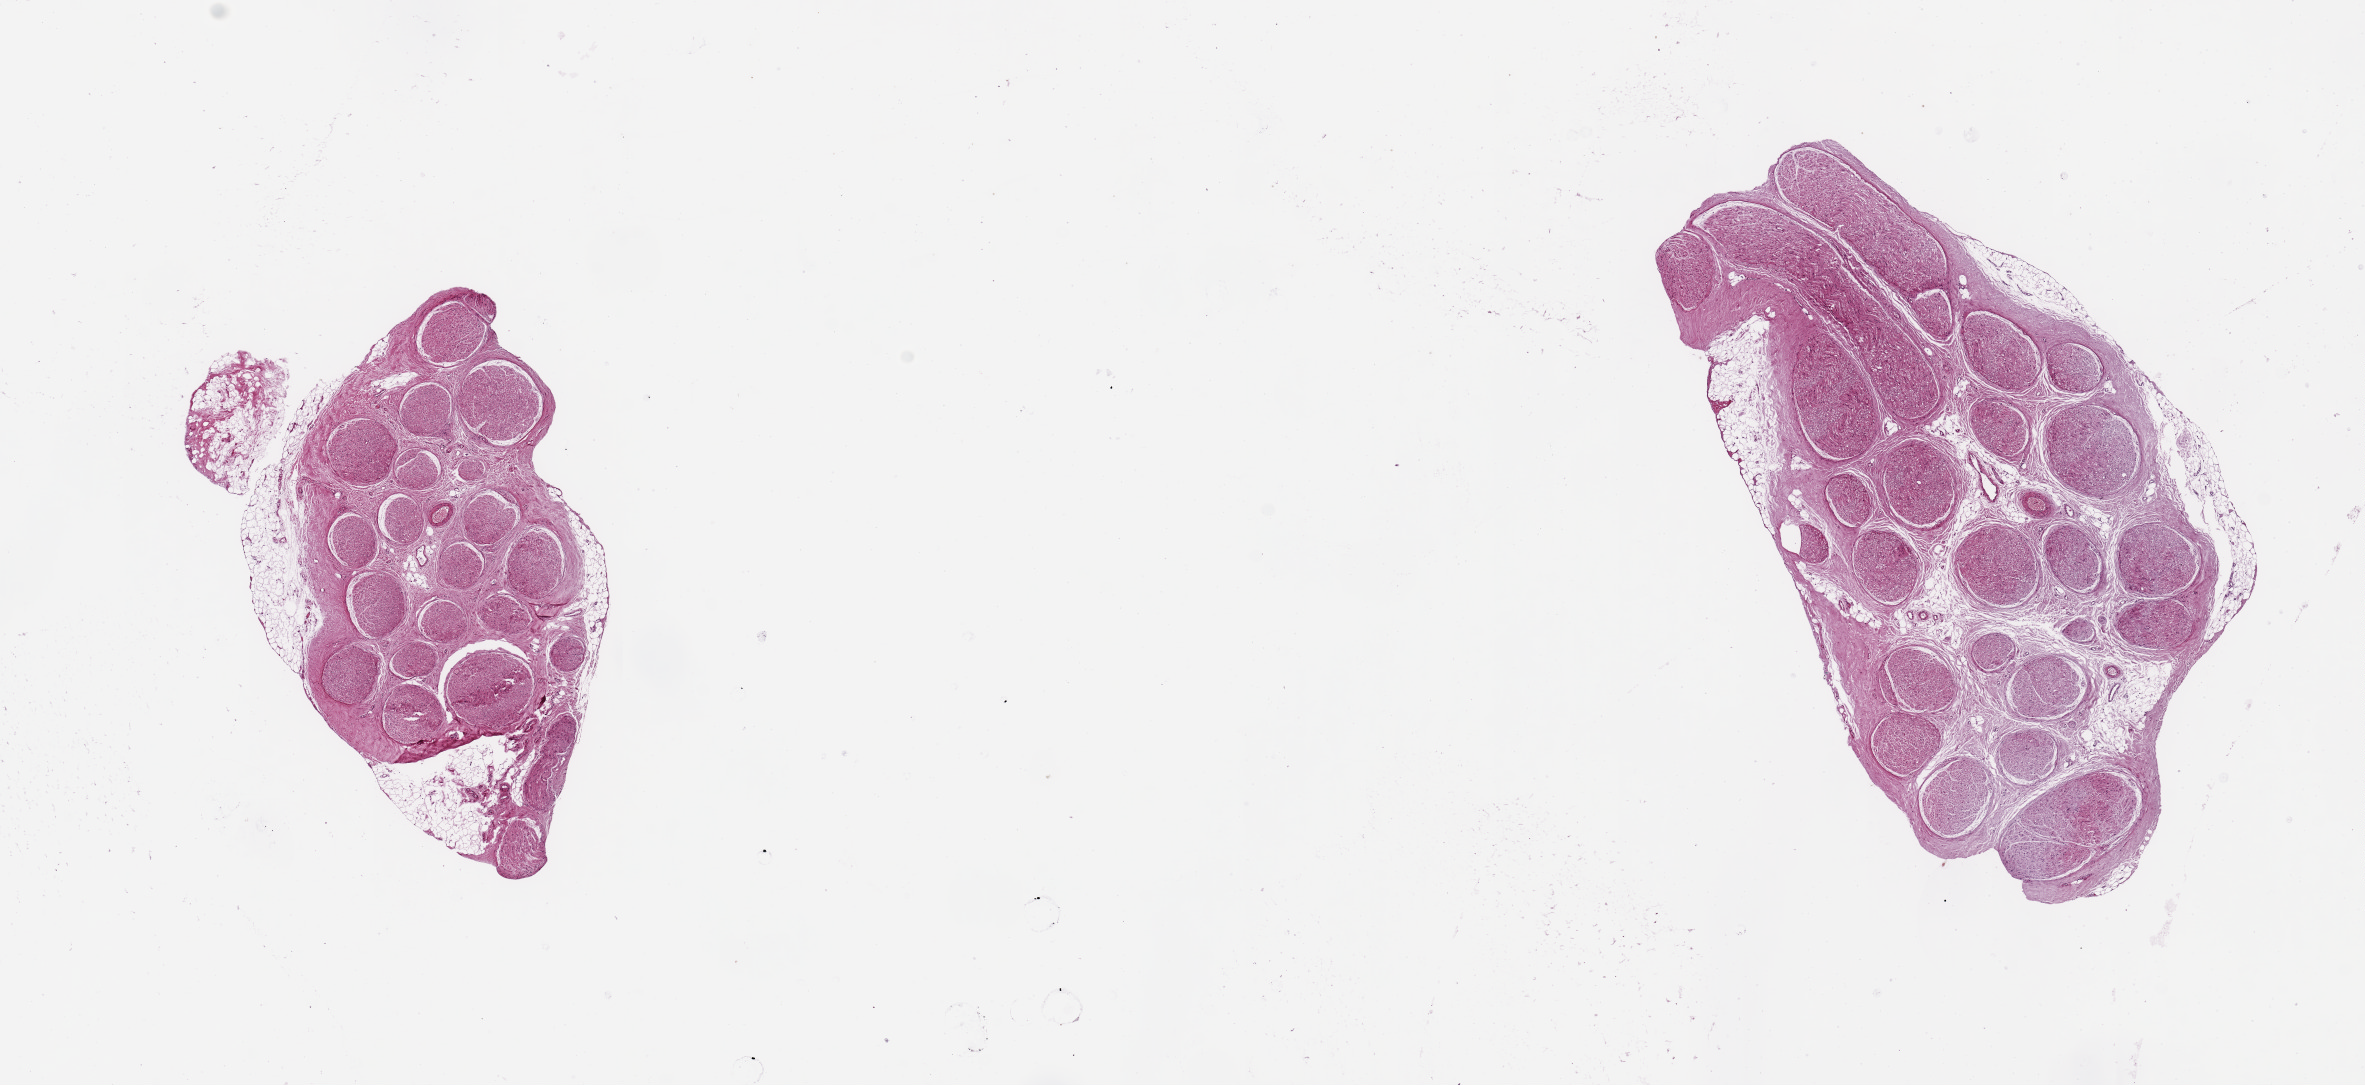
Whole-slide image, hematoxylin and eosin (H&E) stain — a low-resolution overview of the entire scanned area, about 18.7 x 8.6 mm (from a 20x scan). PAXgene-fixed, paraffin-embedded tissue. Section of tibial nerve (target tissue). Donor tissue sample. Donor: male.
Reviewer comment on this tissue sample: 2 pieces, 6x3.5 & 5x3mm; 10-20% surrounding adipose.